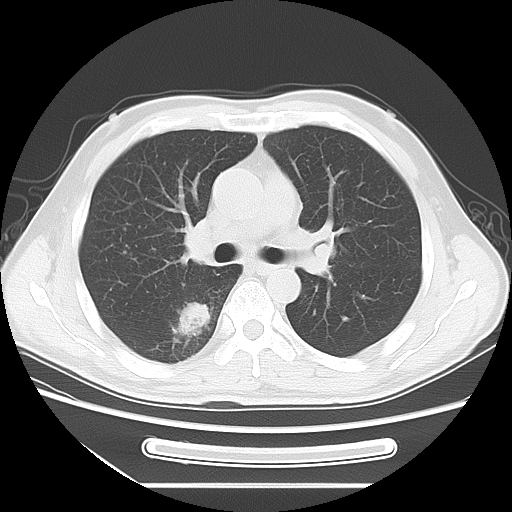
Chest CT, one axial slice. Slice 45 of 71 in the series (ordered by position). Reconstruction kernel LUNG. 120 kVp. Lung window (W 1500 / L -600 HU). 512 × 512 image matrix. Patient: male, 51 years. From the clinical record (not read from this slice): clinical TNM (as recorded): T1c N3 M0.
Annotated regions visible in this slice (rectangle marked by the reading radiologist):
- lung tumour (recorded histology: adenocarcinoma): bounding box [x1, y1, x2, y2] px = [291, 209, 336, 278]